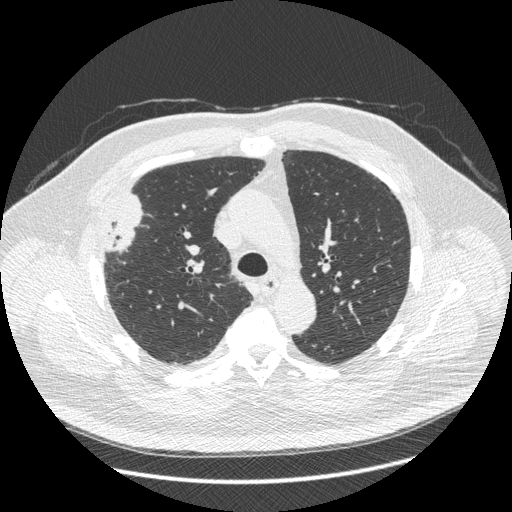
Axial slice from a low-dose chest CT screening exam. Third screening round (two years after baseline). Lung window (W 1500 / L -600 HU). 1.25 mm slice thickness. Male participant, aged 66 years at enrolment. Current smoker at enrolment.
Lesion marked by an expert reader, box from (x=87, y=198) to (x=147, y=268) px. Screening reader's record for this exam (one nodule recorded; not confirmed to be the boxed lesion): non-calcified nodule or mass ≥4 mm, right upper lobe, 48 × 25 mm, spiculated (stellate) margins, soft tissue attenuation, pre-existing on the prior screen: no. Participant outcome: lung cancer diagnosed 35 days after this screen — non-small cell carcinoma, right upper lobe, stage IV (AJCC 6th edition), 50 mm at pathology.